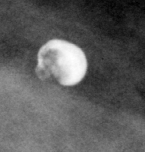
Cropped region of a digitized screen-film mammogram centred on a radiologist-marked abnormality; left breast; MLO view; BI-RADS breast density category 2 (scale 1–4).
- Finding: calcifications, morphology vascular / coarse / lucent centered; BI-RADS assessment category 2; subtlety rating 5 on a 1 (subtle) to 5 (obvious) scale; benign; no additional work-up was recommended (benign without callback).